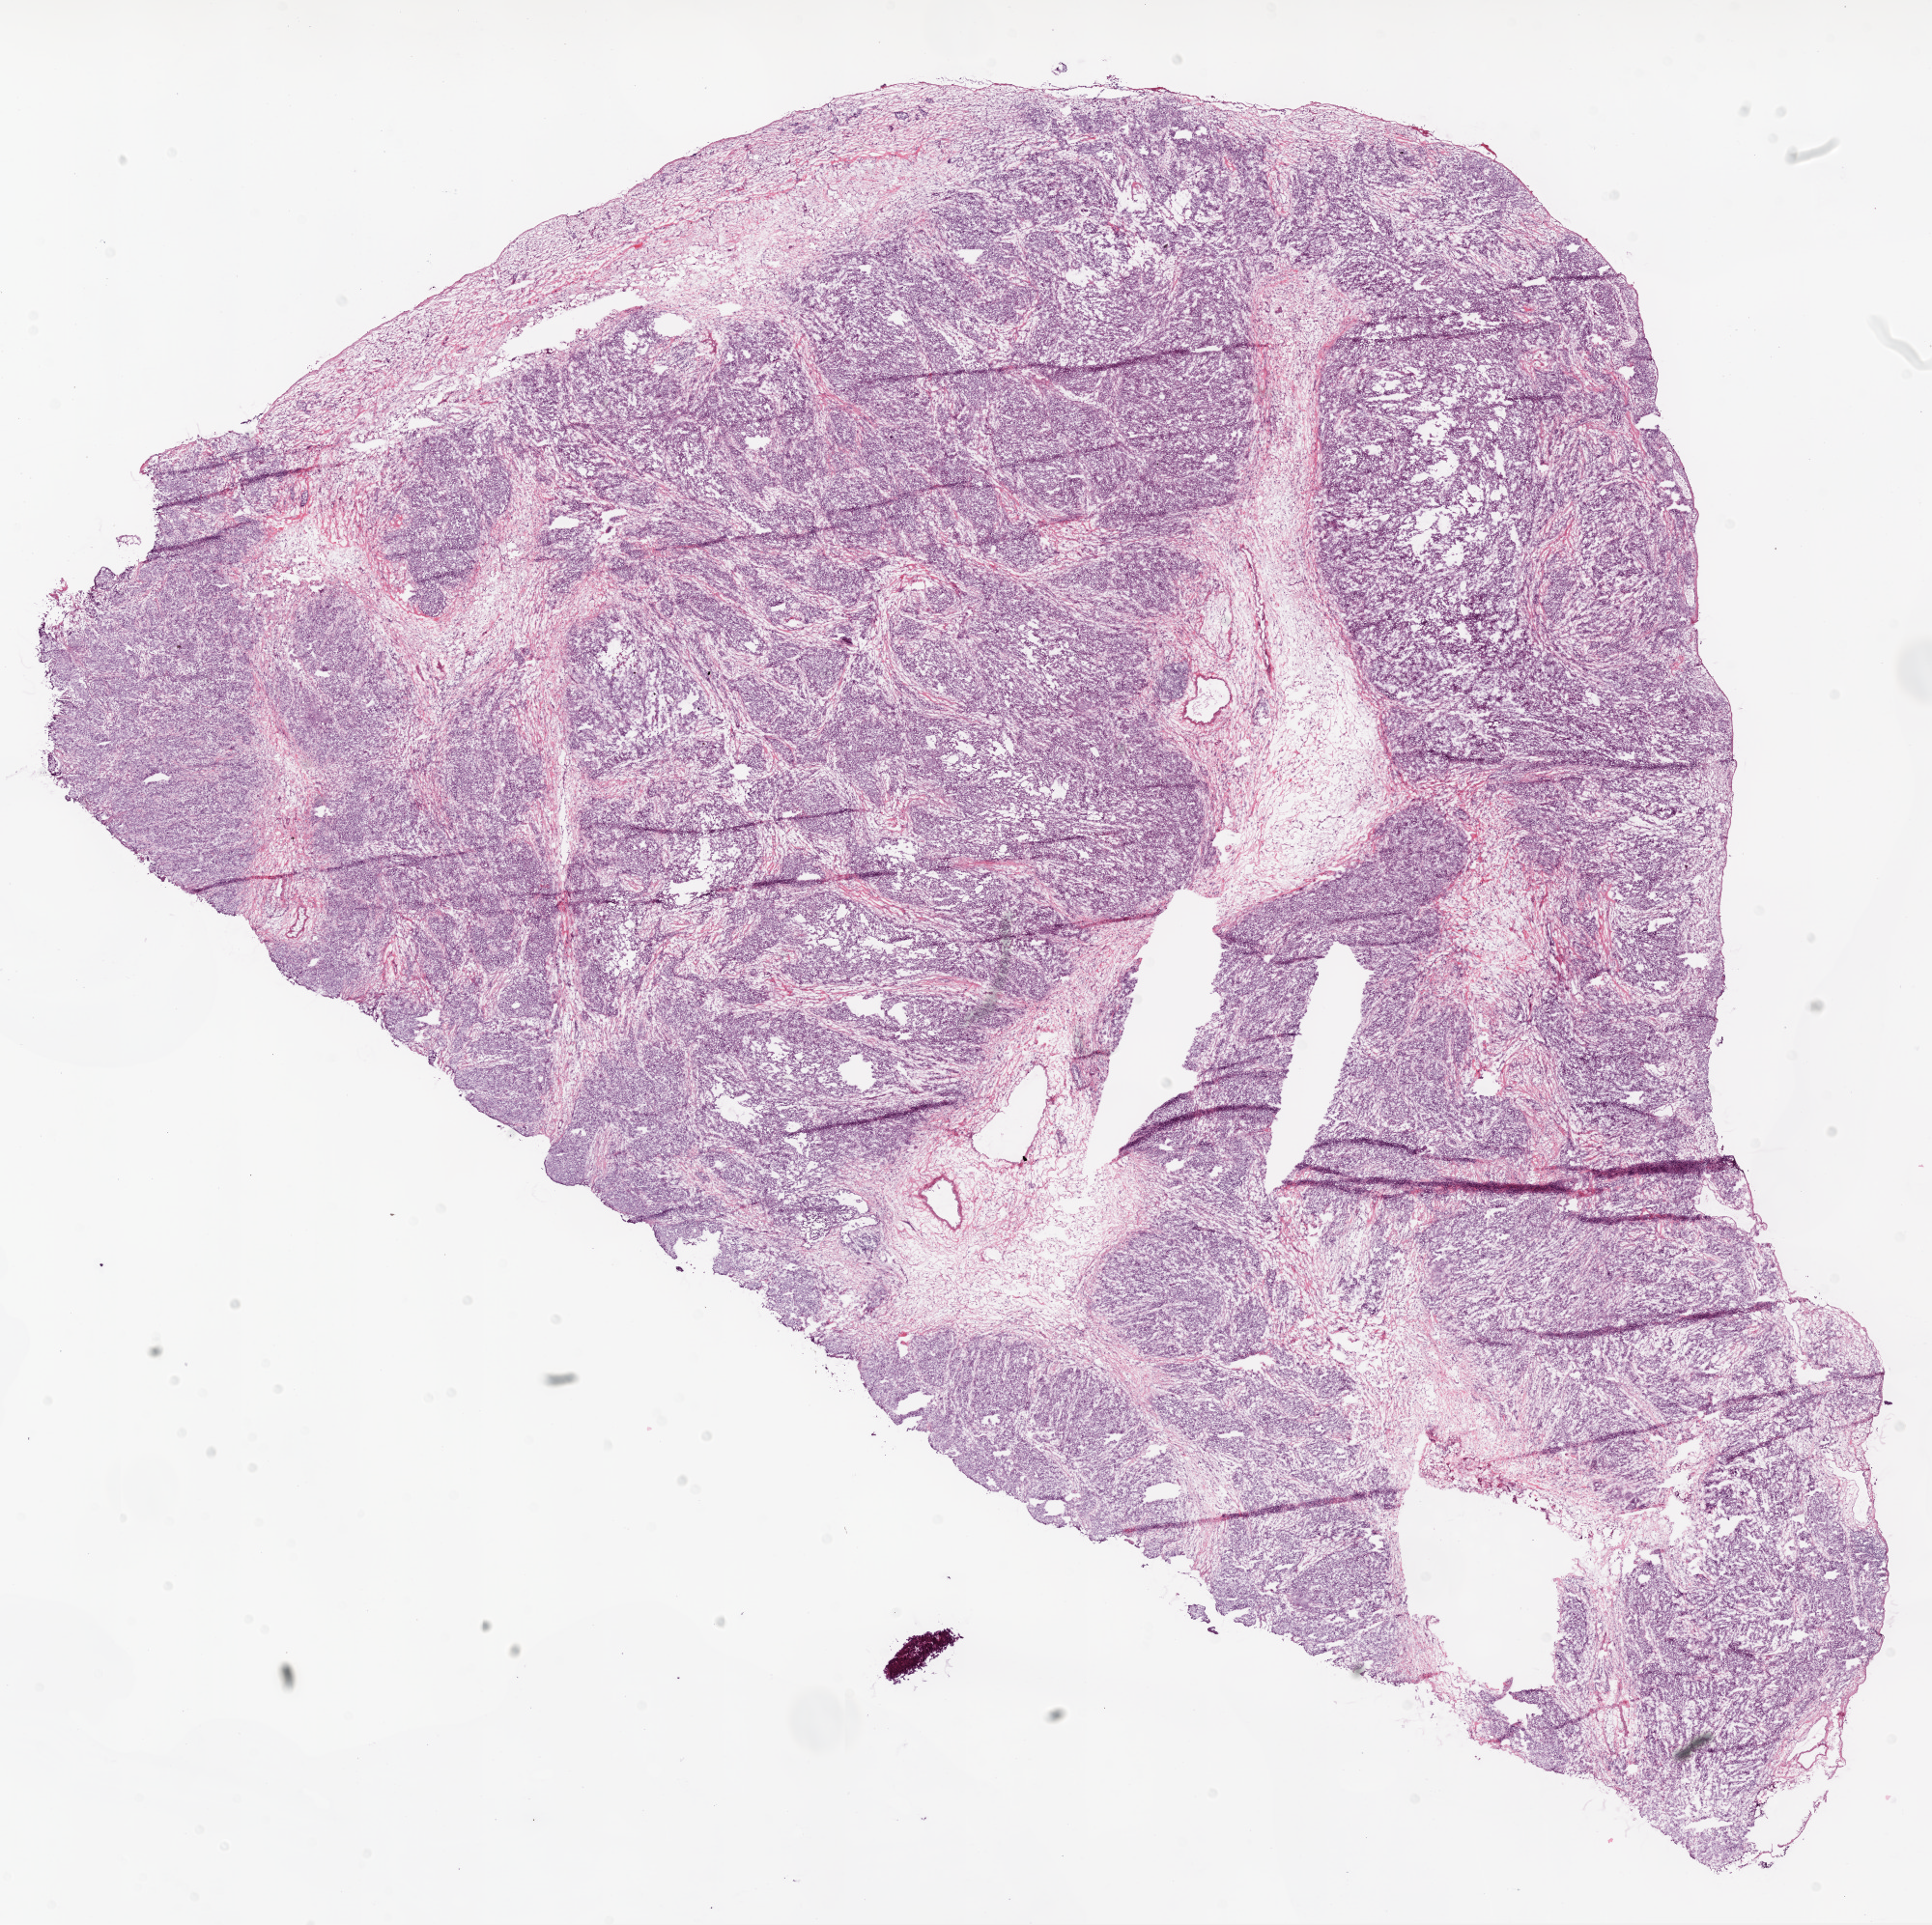
Whole-slide histology image, Hematoxylin and eosin (H&E) stained, low-resolution overview of the scanned area, about 16.0 x 16.0 mm, frozen section, sample: primary tumour, ovary. Female patient; age at initial diagnosis 54 years. Histologic grade: G2 (moderately differentiated). Slide review estimates, as recorded: tumour cells 90%, tumour nuclei 80%, normal cells 0%, stromal cells 0%, necrosis 10%. Inflammatory infiltration, as recorded: lymphocyte infiltration 10%.
Pathologic diagnosis: Serous cystadenocarcinoma, NOS. FIGO stage: IIIC.